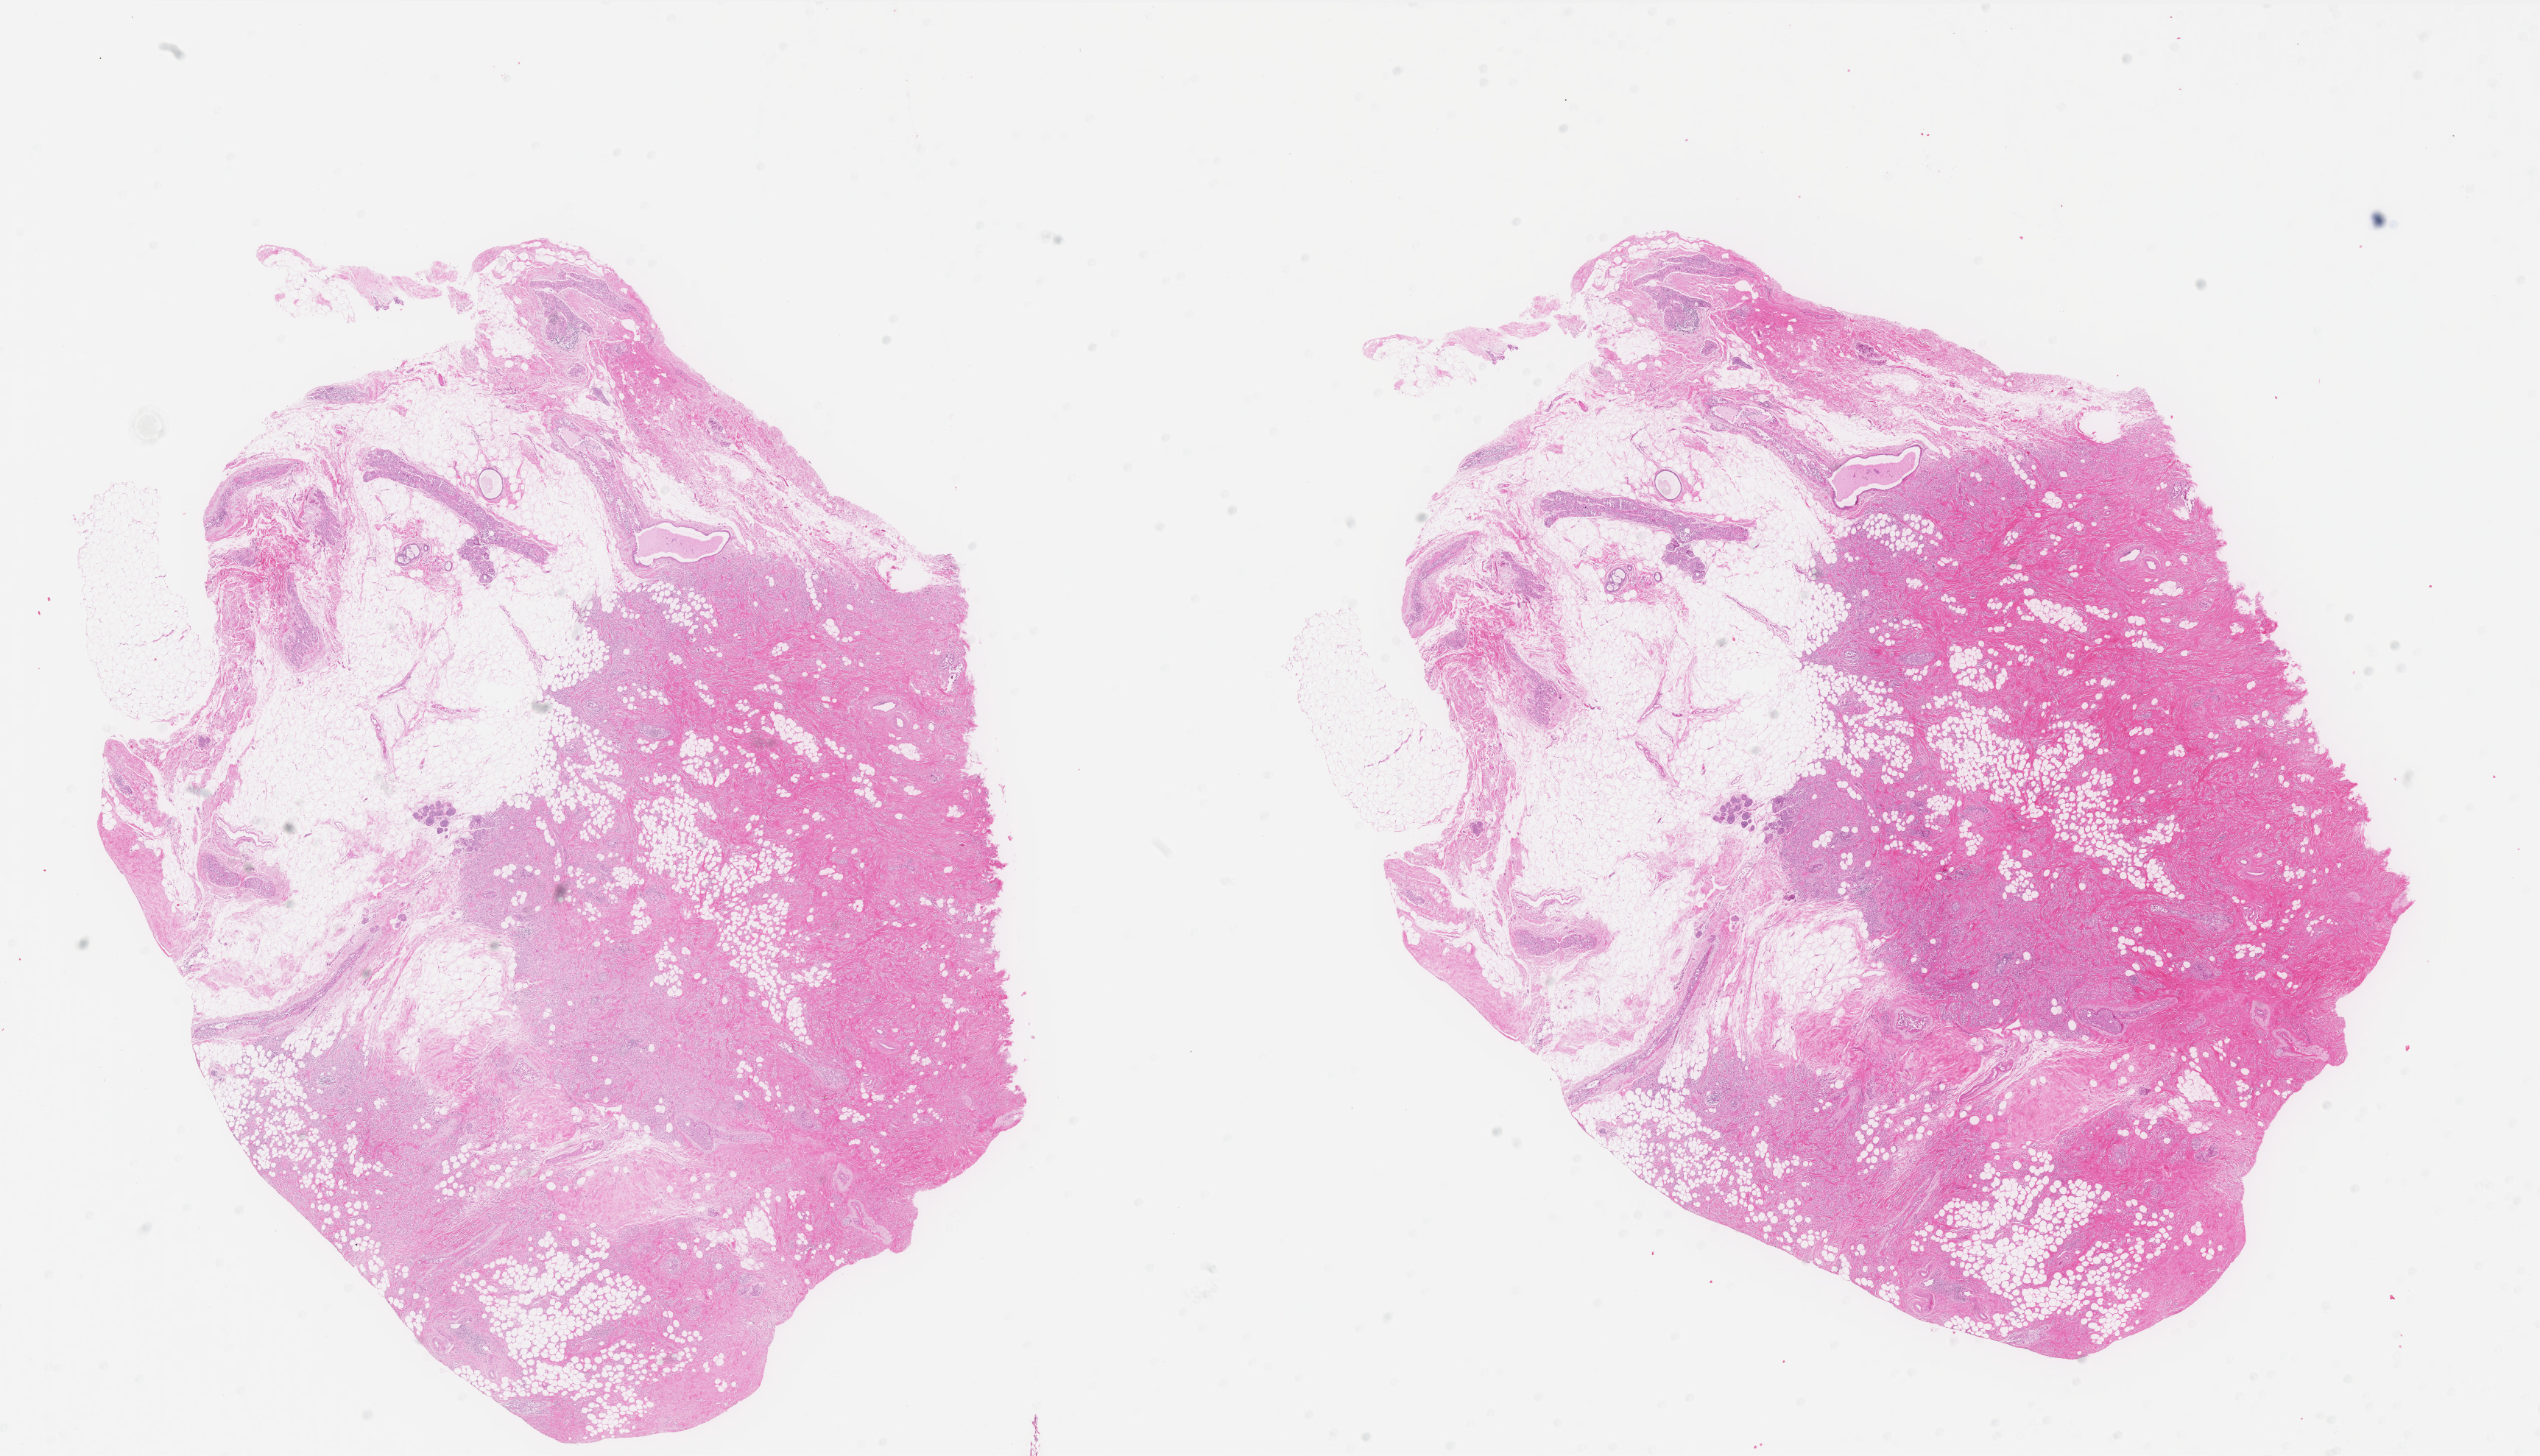
Whole-slide histology image, H&E — shown as a low-resolution overview of the whole scanned area (about 27.7 x 15.9 mm, acquisition: 40x scan); formalin-fixed paraffin-embedded (FFPE) diagnostic section; primary tumour sample from the breast. Patient sex: female.
Histologic diagnosis: Lobular carcinoma, NOS. AJCC pathologic stage: IIB.